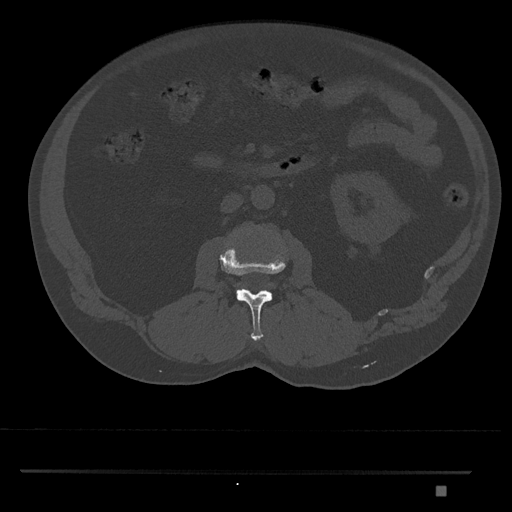
CT including the spine, one axial slice. Slice 734 of 1134 in the series (ordered by position). 120 kVp. Bone window (W 1800 / L 400 HU). 0.5 mm slice thickness. 512 × 512 image matrix, field of view 429 × 429 mm. Male patient, age 65 years. Case-level facts recorded for this patient, not image findings: primary cancer: prostate.
Structures marked on this image (semi-automatic segmentation, software-assisted and operator-edited):
- L2 vertebra: bounding box [x1, y1, x2, y2] px = [219, 243, 286, 341]